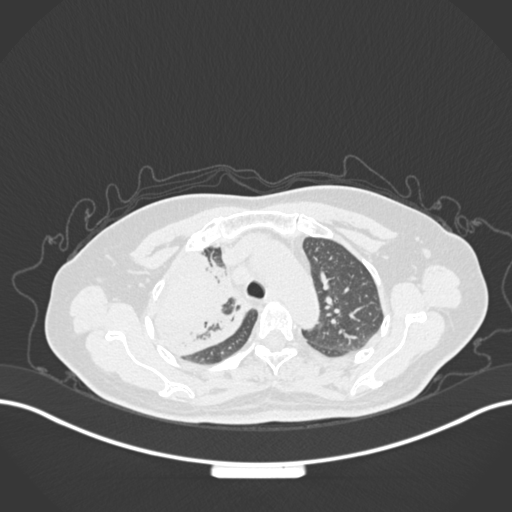
Chest CT, one axial slice; slice 119 of 177 in the series (ordered by position); 120 kVp; lung window (W 1500 / L -600 HU); 1 mm slice thickness; 512 × 512 image matrix, field of view 400 × 400 mm. Patient: female, 60 years. Case-level facts recorded for this patient, not image findings: clinical TNM (as recorded): T3 N1 M1.
Structures marked on this image (bounding box drawn by a radiologist):
- lung tumour (recorded histology: adenocarcinoma): box from (x=147, y=246) to (x=250, y=357) px